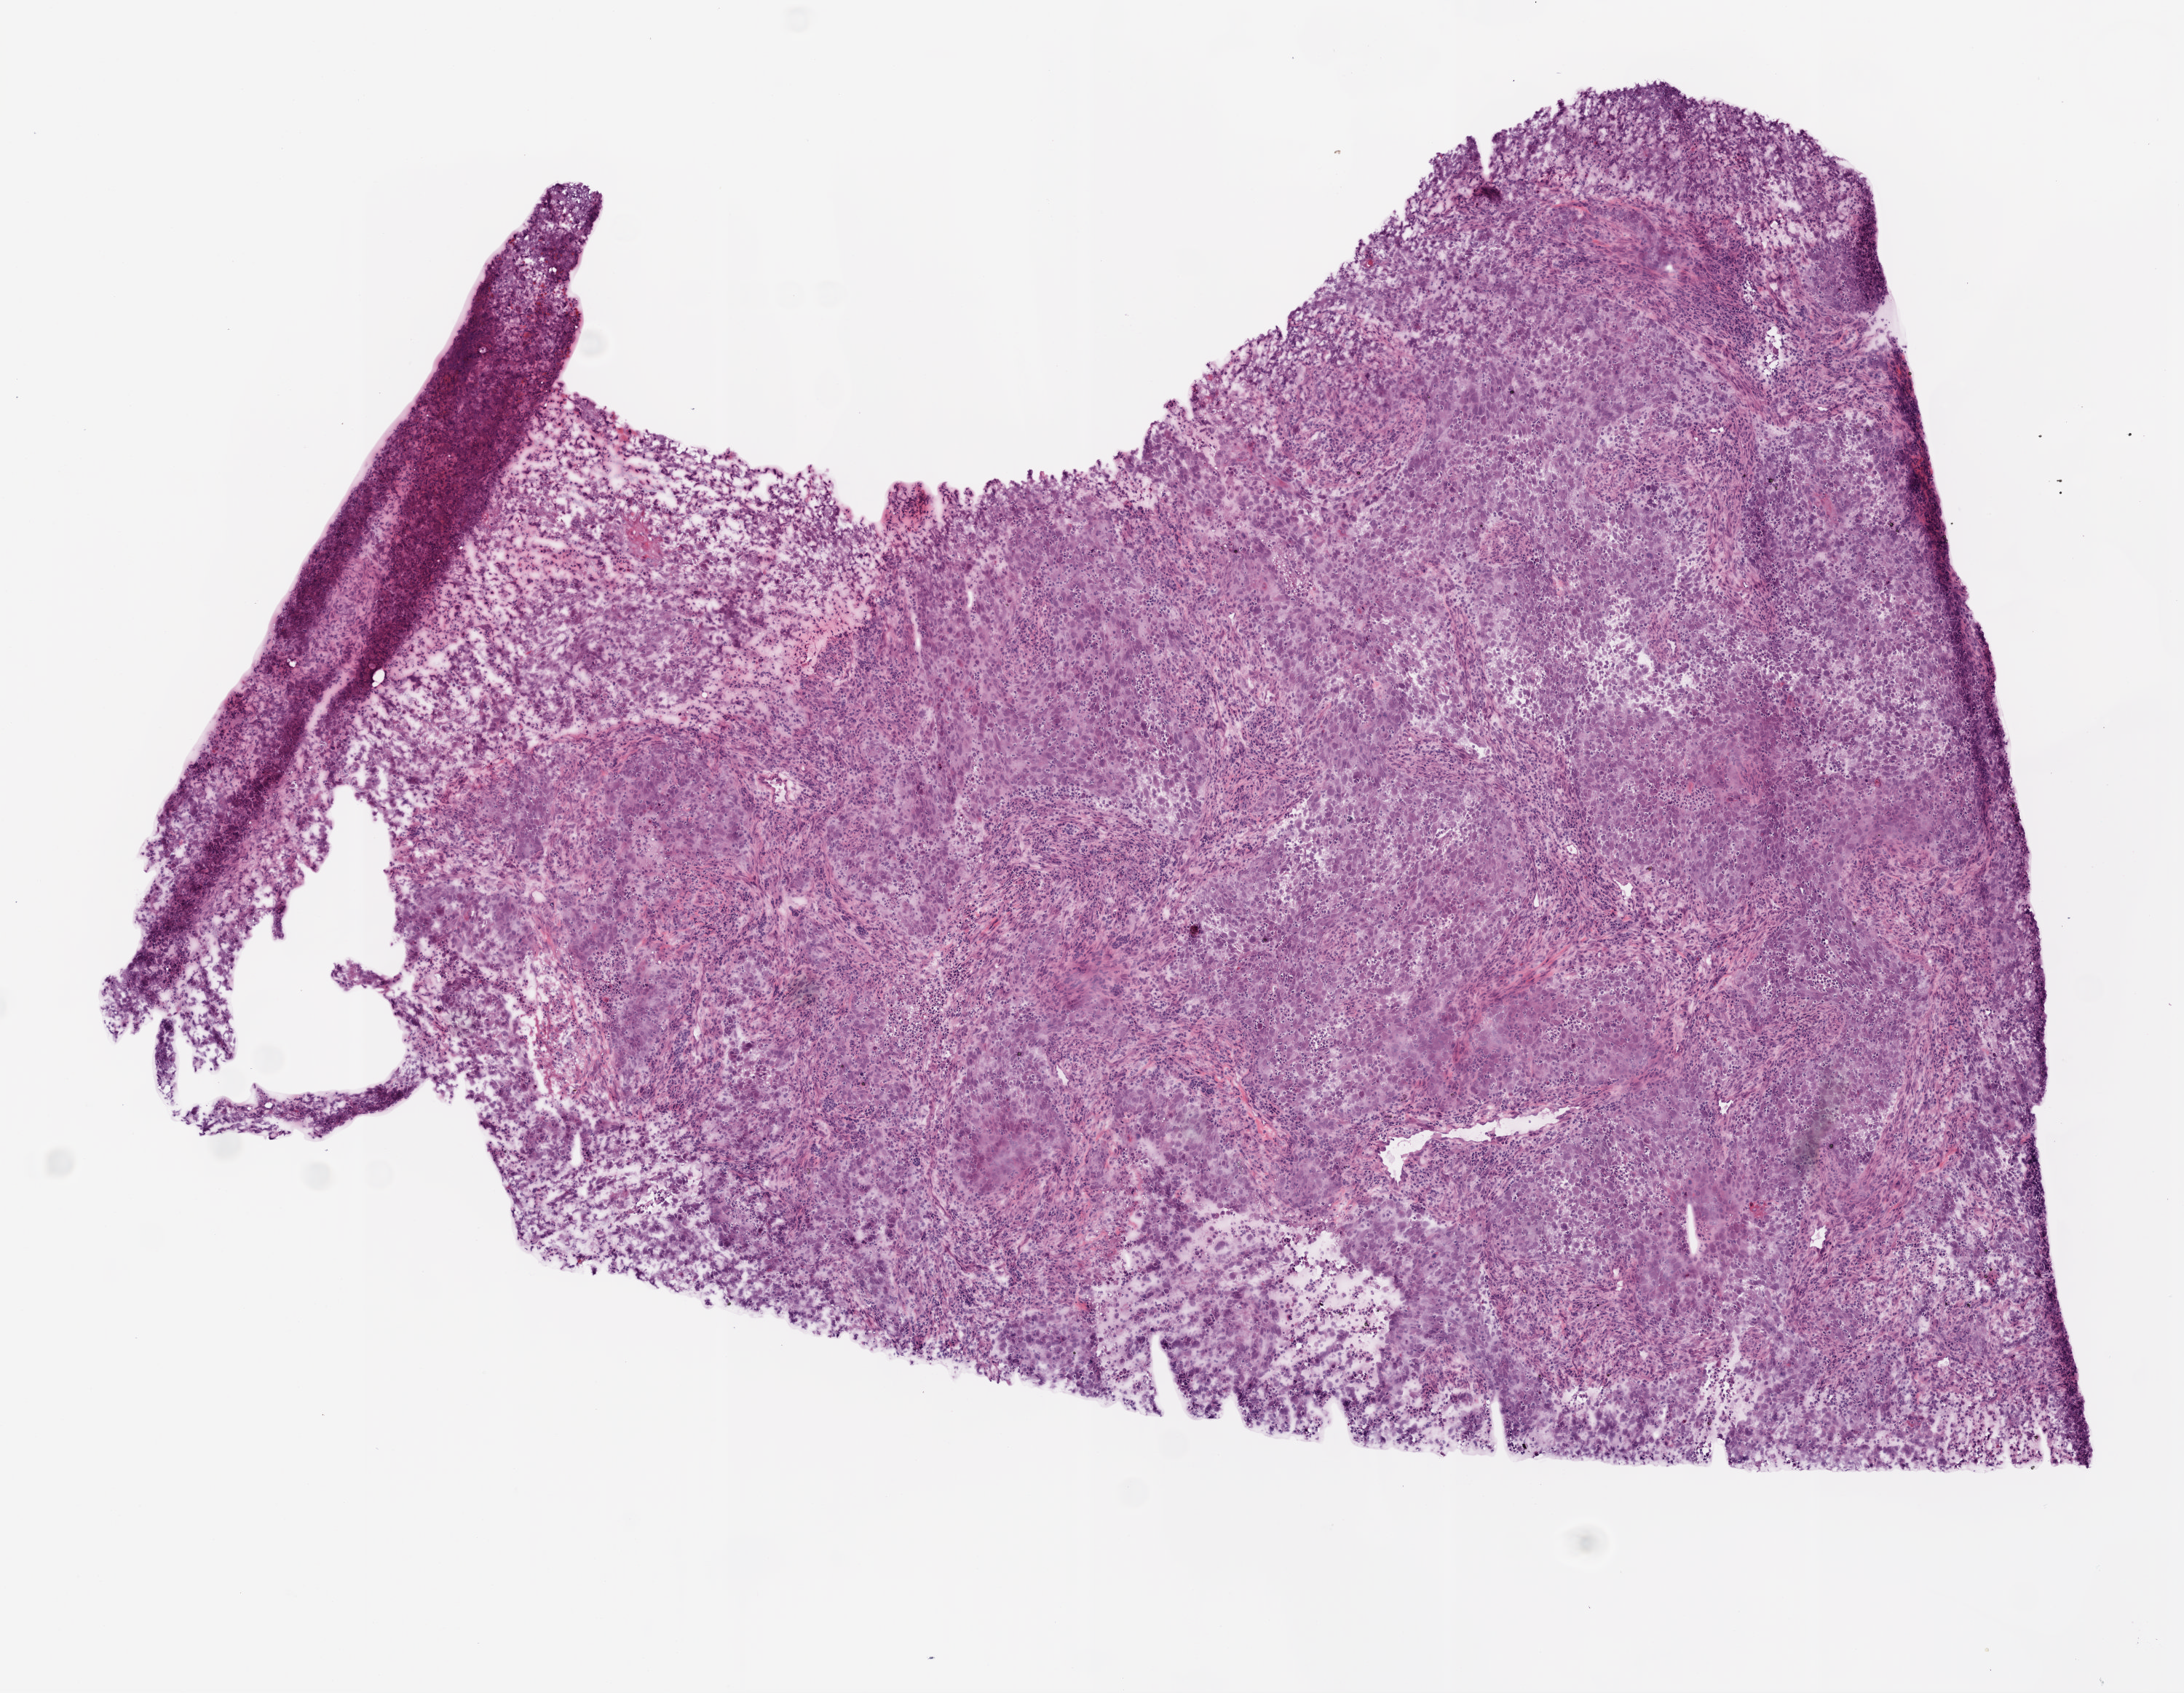
Whole-slide histology image, Hematoxylin and eosin (H&E) stained, whole scanned area (about 6.0 x 4.7 mm, acquisition: 20x scan) shown as a low-resolution overview; frozen section from the top of the tissue portion; lung, primary tumour sample. Patient: male, age at initial diagnosis 63 years. Slide review estimates, as recorded: tumour cells 80%, tumour nuclei 85%, normal cells 0%, stromal cells 5%, necrosis 15%.
AJCC pathologic stage: IB (5th edition). Diagnosis: Squamous cell carcinoma, NOS.